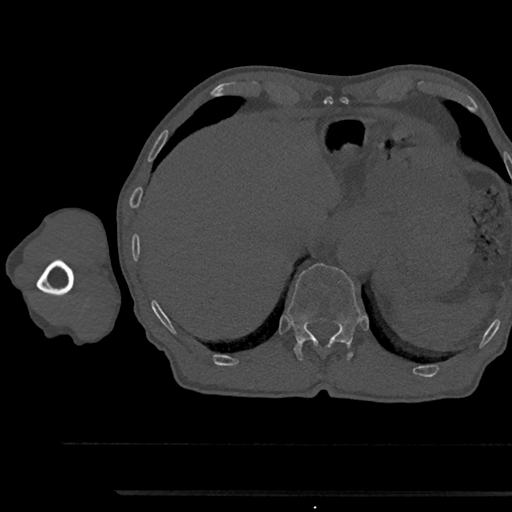
CT including the spine, one axial slice. Slice 738 of 797 in the series (ordered by position). Reconstruction kernel Br40s/3. Bone window (W 1800 / L 400 HU). 0.5 mm slice thickness. 512 × 512 image matrix. Patient: male, 79 years. From the clinical record (not read from this slice): primary cancer: prostate.
Annotated regions visible in this slice (semi-automatic segmentation, software-assisted and operator-edited):
- T12 vertebra: bounding box <287,263,360,361> (left, top, right, bottom; pixels)